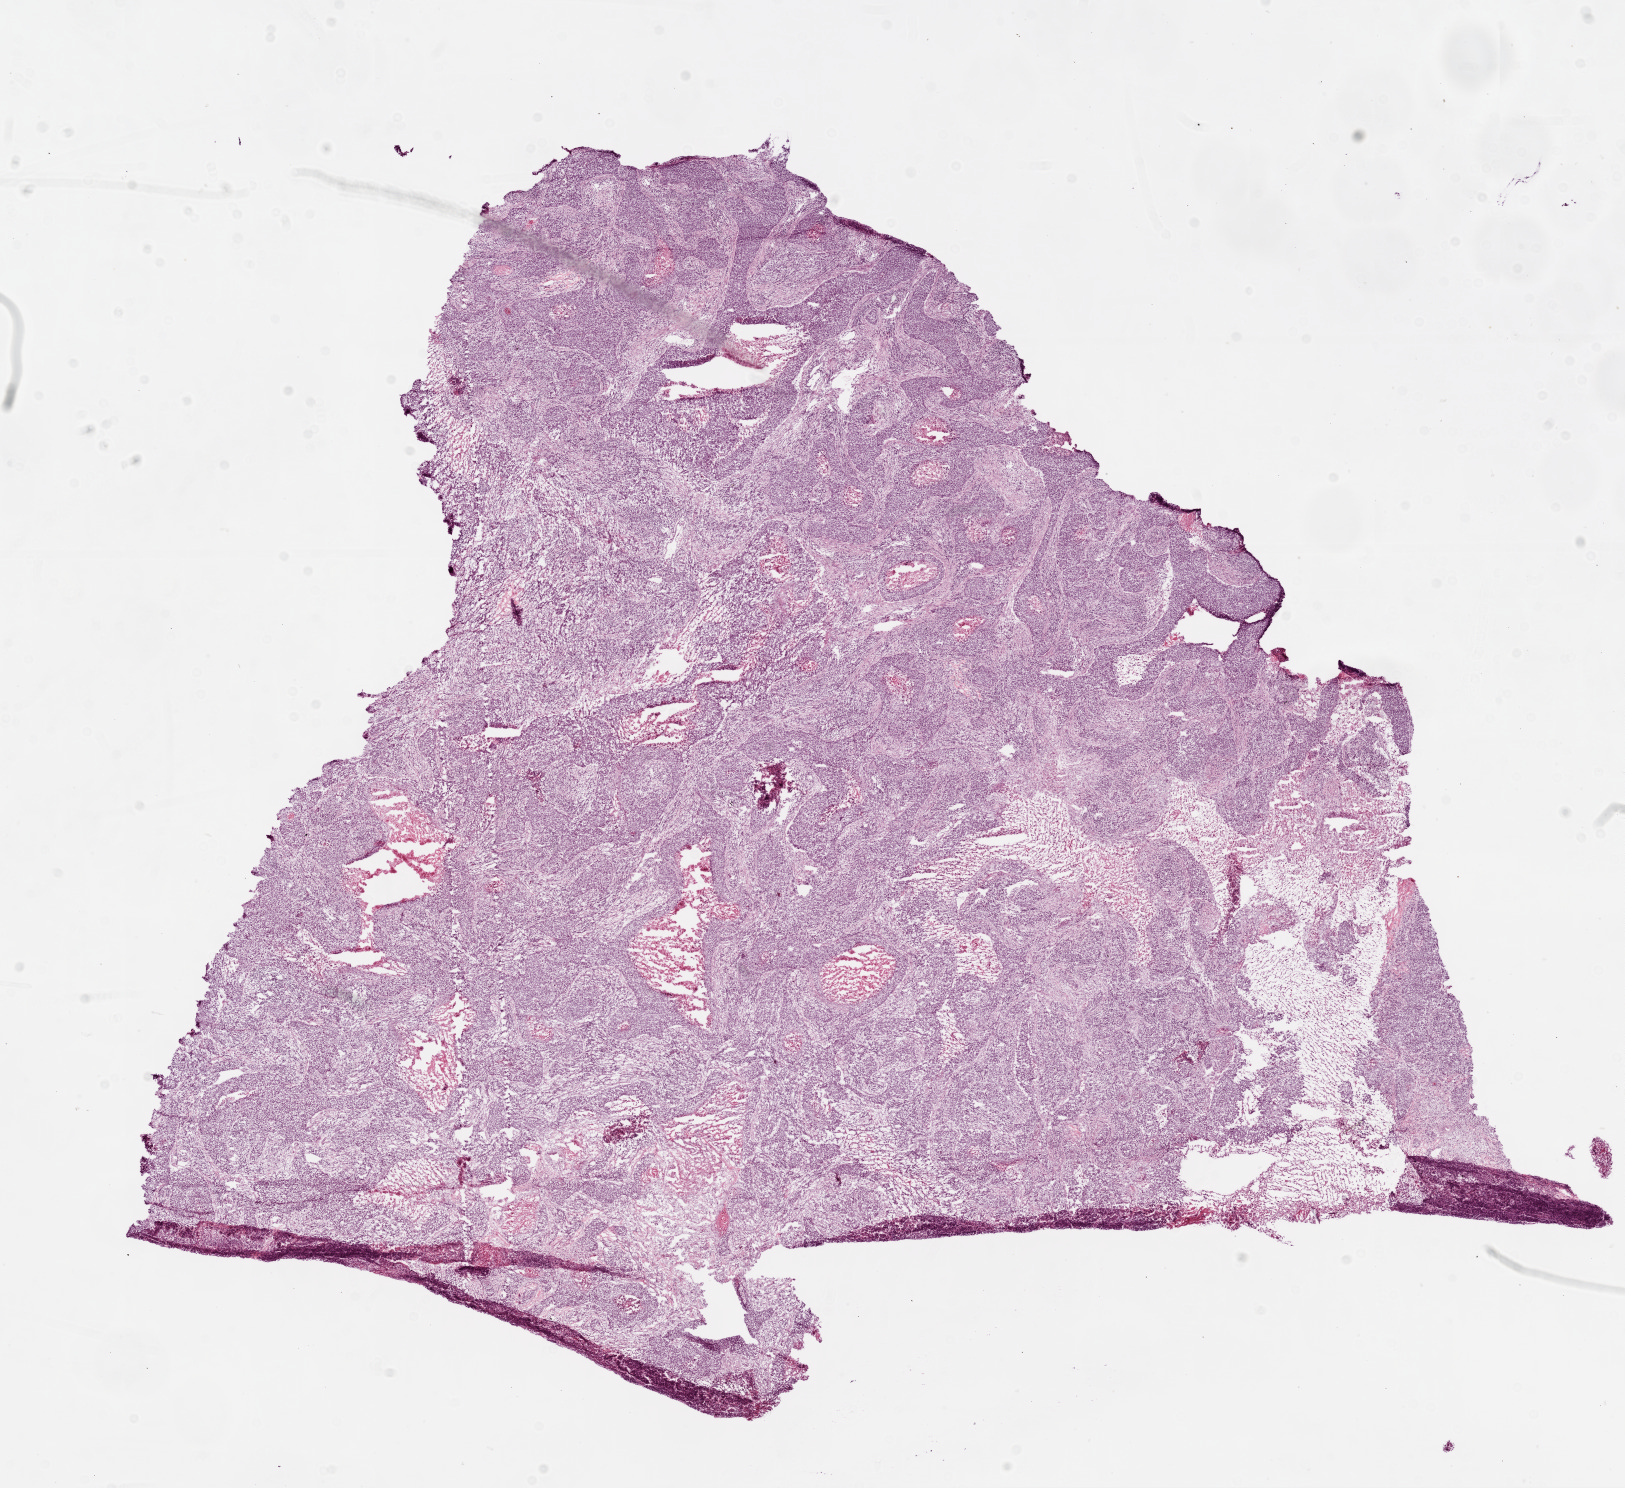
Hematoxylin and eosin (H&E) stained whole-slide image, whole scanned area (about 13.0 x 11.9 mm, slide scanned at 20x) shown as a low-resolution overview; frozen section; primary tumour sample from the lung. Female patient; age at initial diagnosis 79 years. Slide review estimates, as recorded: tumour cells 75%, tumour nuclei 85%, normal cells 0%, stromal cells 10%, necrosis 15%.
• AJCC pathologic stage: IIB
• pathologic diagnosis: Squamous cell carcinoma, NOS (upper lobe, lung)
• TNM: T2 N1 M0